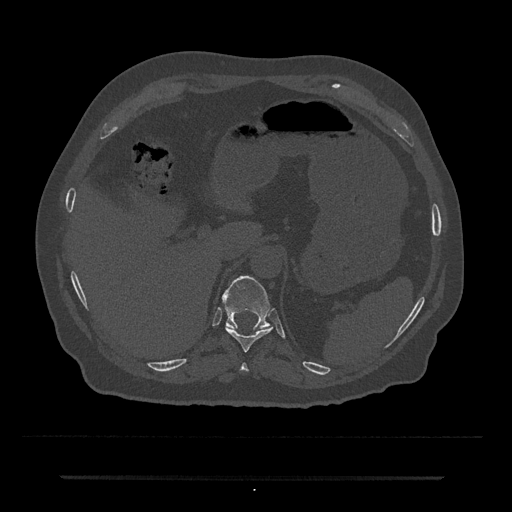
CT including the spine, one axial slice. Slice 210 of 797 in the series (ordered by position). Reconstruction kernel Br40s/3. 120 kVp. Bone window (W 1800 / L 400 HU). 512 × 512 image matrix. Male patient, age 69 years. From the clinical record (not read from this slice): primary cancer: prostate.
Structures marked on this image (semi-automatic segmentation, software-assisted and operator-edited):
- T10 vertebra: box from (x=225, y=326) to (x=272, y=352) px
- T11 vertebra: (x=222, y=275)–(x=271, y=330)
- T9 vertebra: (x=240, y=362)–(x=248, y=372)